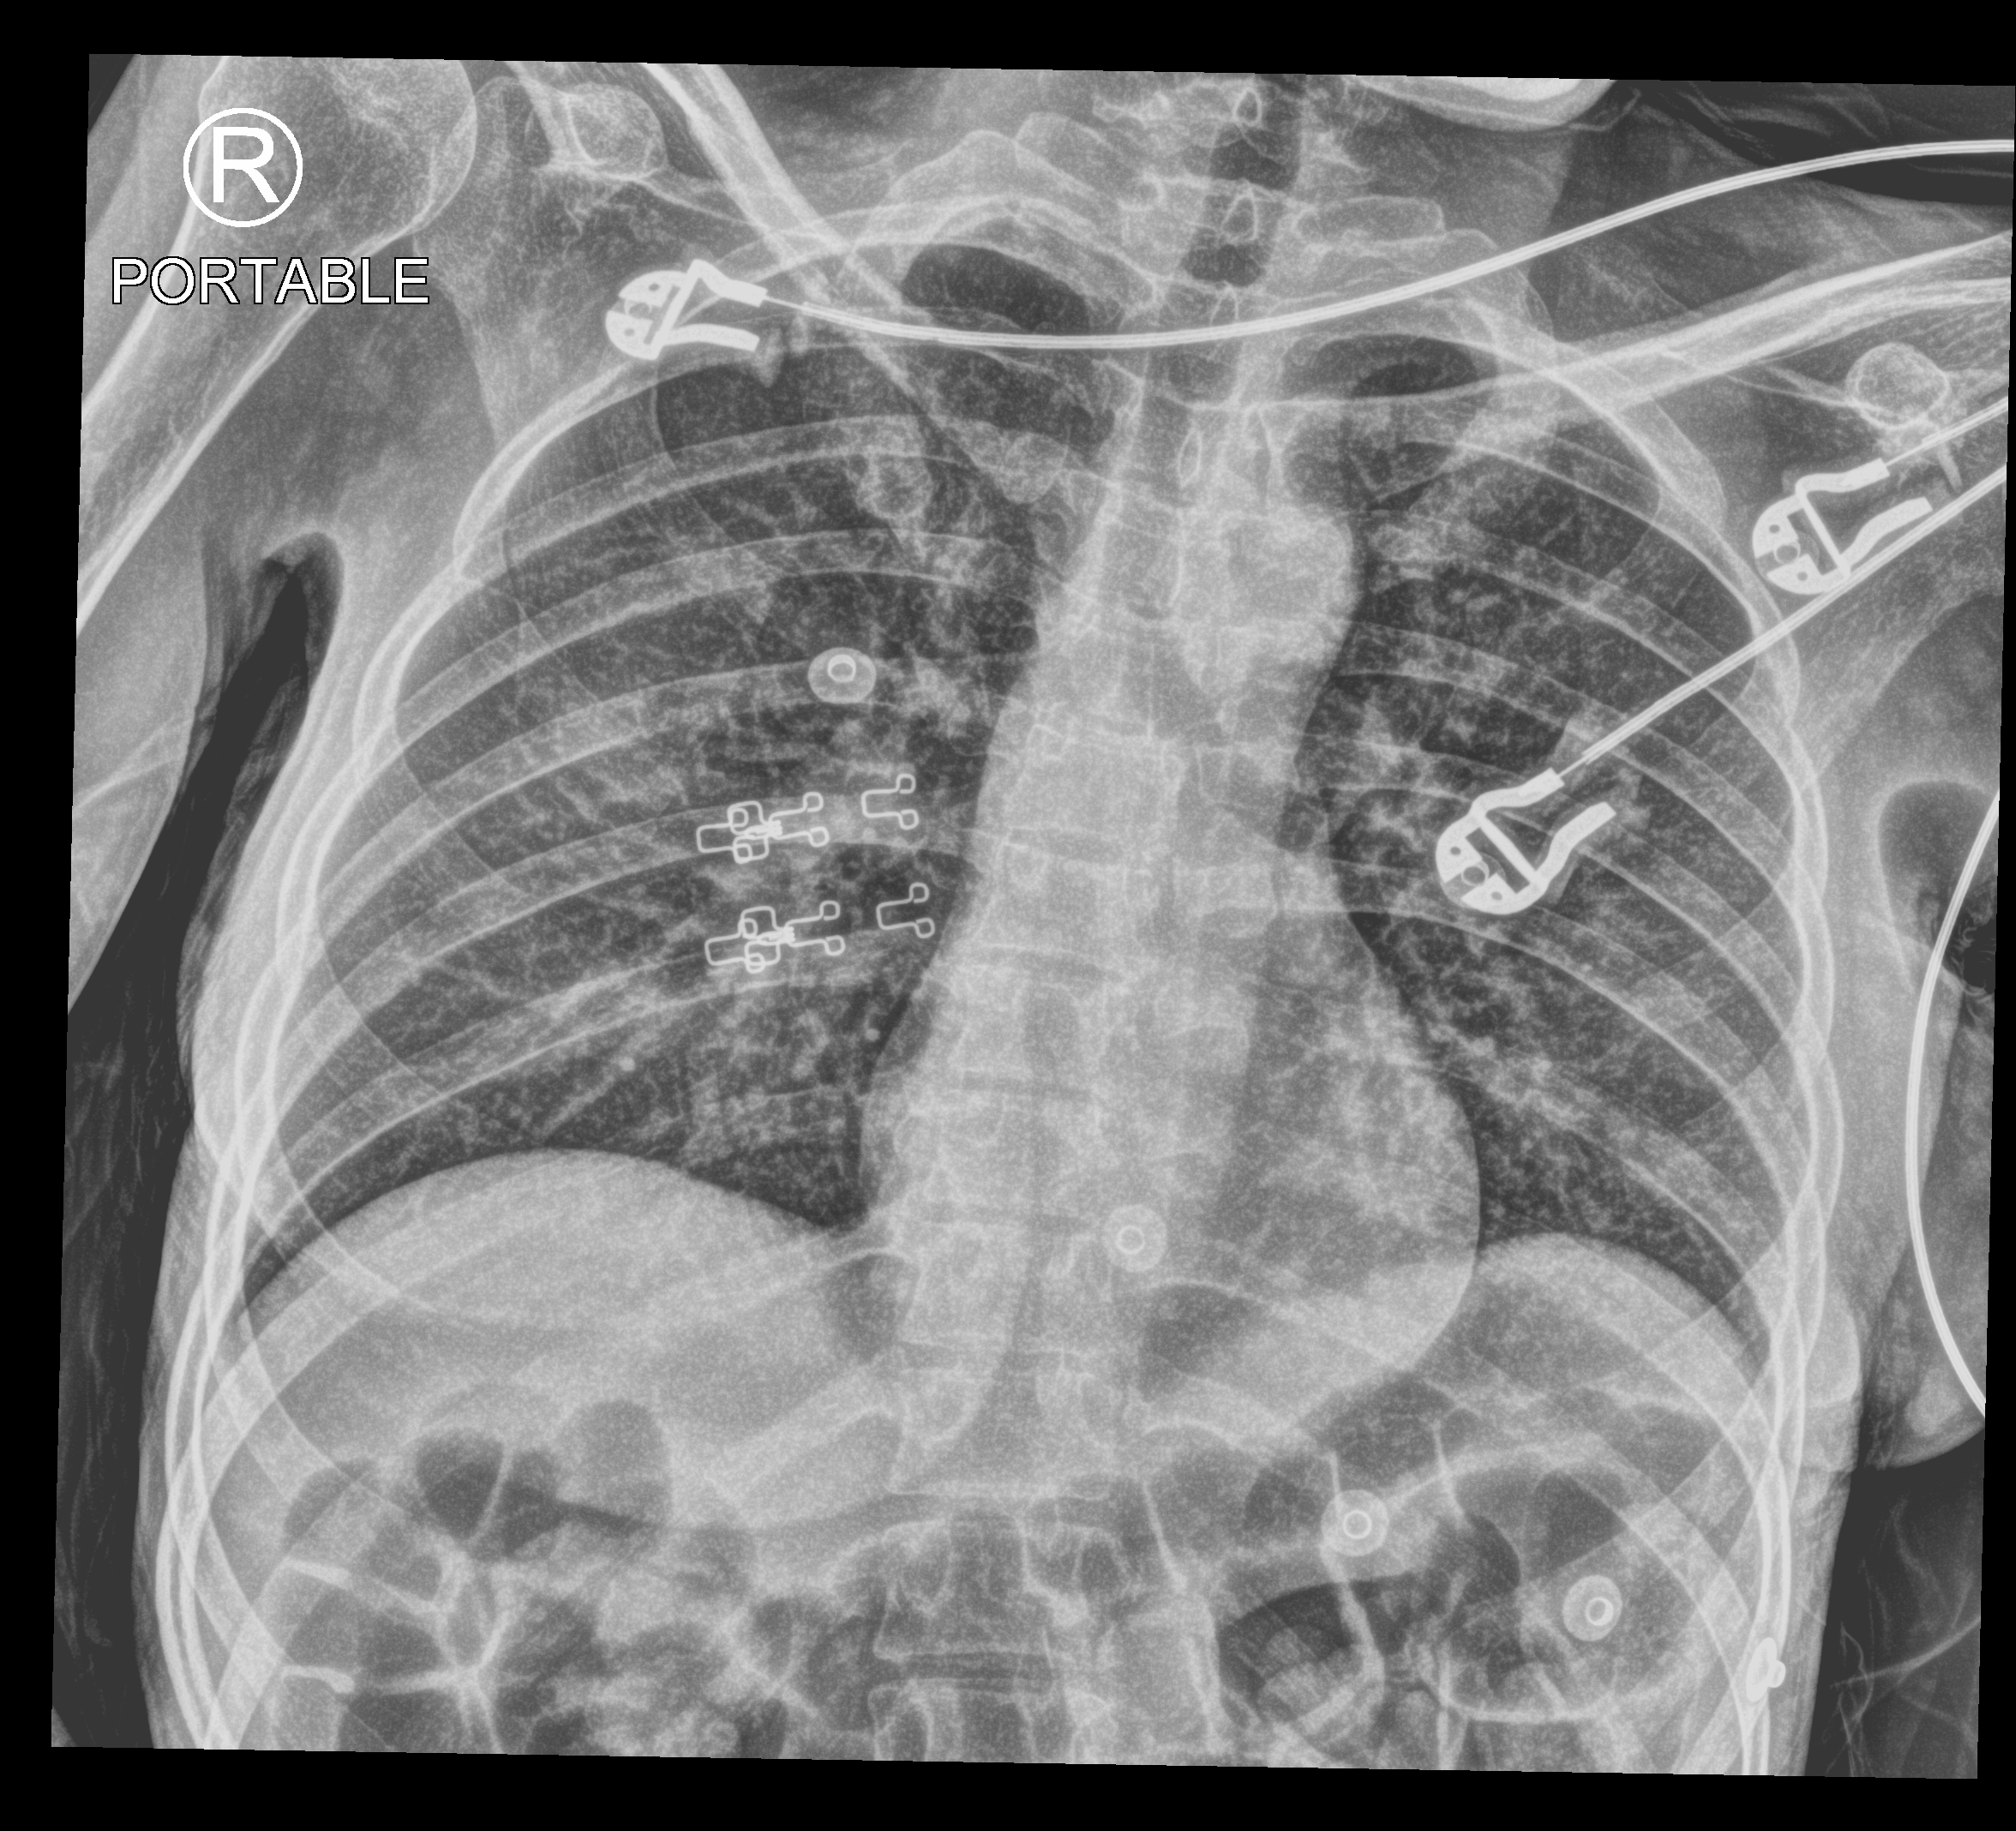
Portable chest radiograph; anteroposterior (AP) projection. Patient hospitalised with COVID-19; female, aged 18–59 years.
Hospital-stay facts (about this admission, not read from this image; timing relative to this image not recorded): length of hospital stay: 4 days; mechanically ventilated during this hospital stay: no.